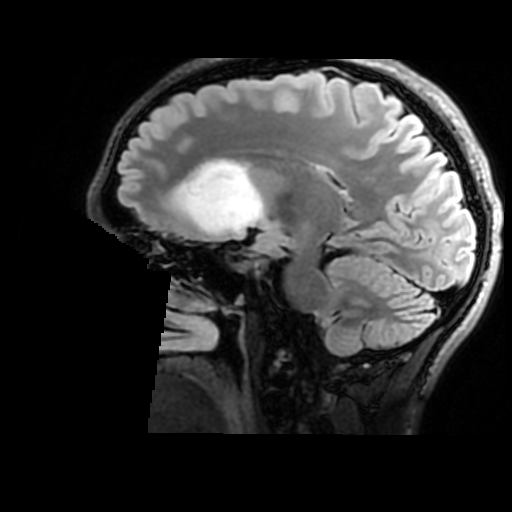
Brain MRI from a brain-tumour surgery series, one sagittal slice. Position 102 of 176 along the scan axis. T2 FLAIR. 512 × 512 image matrix, field of view 240 × 240 mm. From the clinical record (not read from this slice): histopathology: Astrocytoma; WHO grade: 2.
Structures marked on this image (expert manual segmentation):
- tumour: bounding box [x1, y1, x2, y2] px = [175, 159, 264, 233]